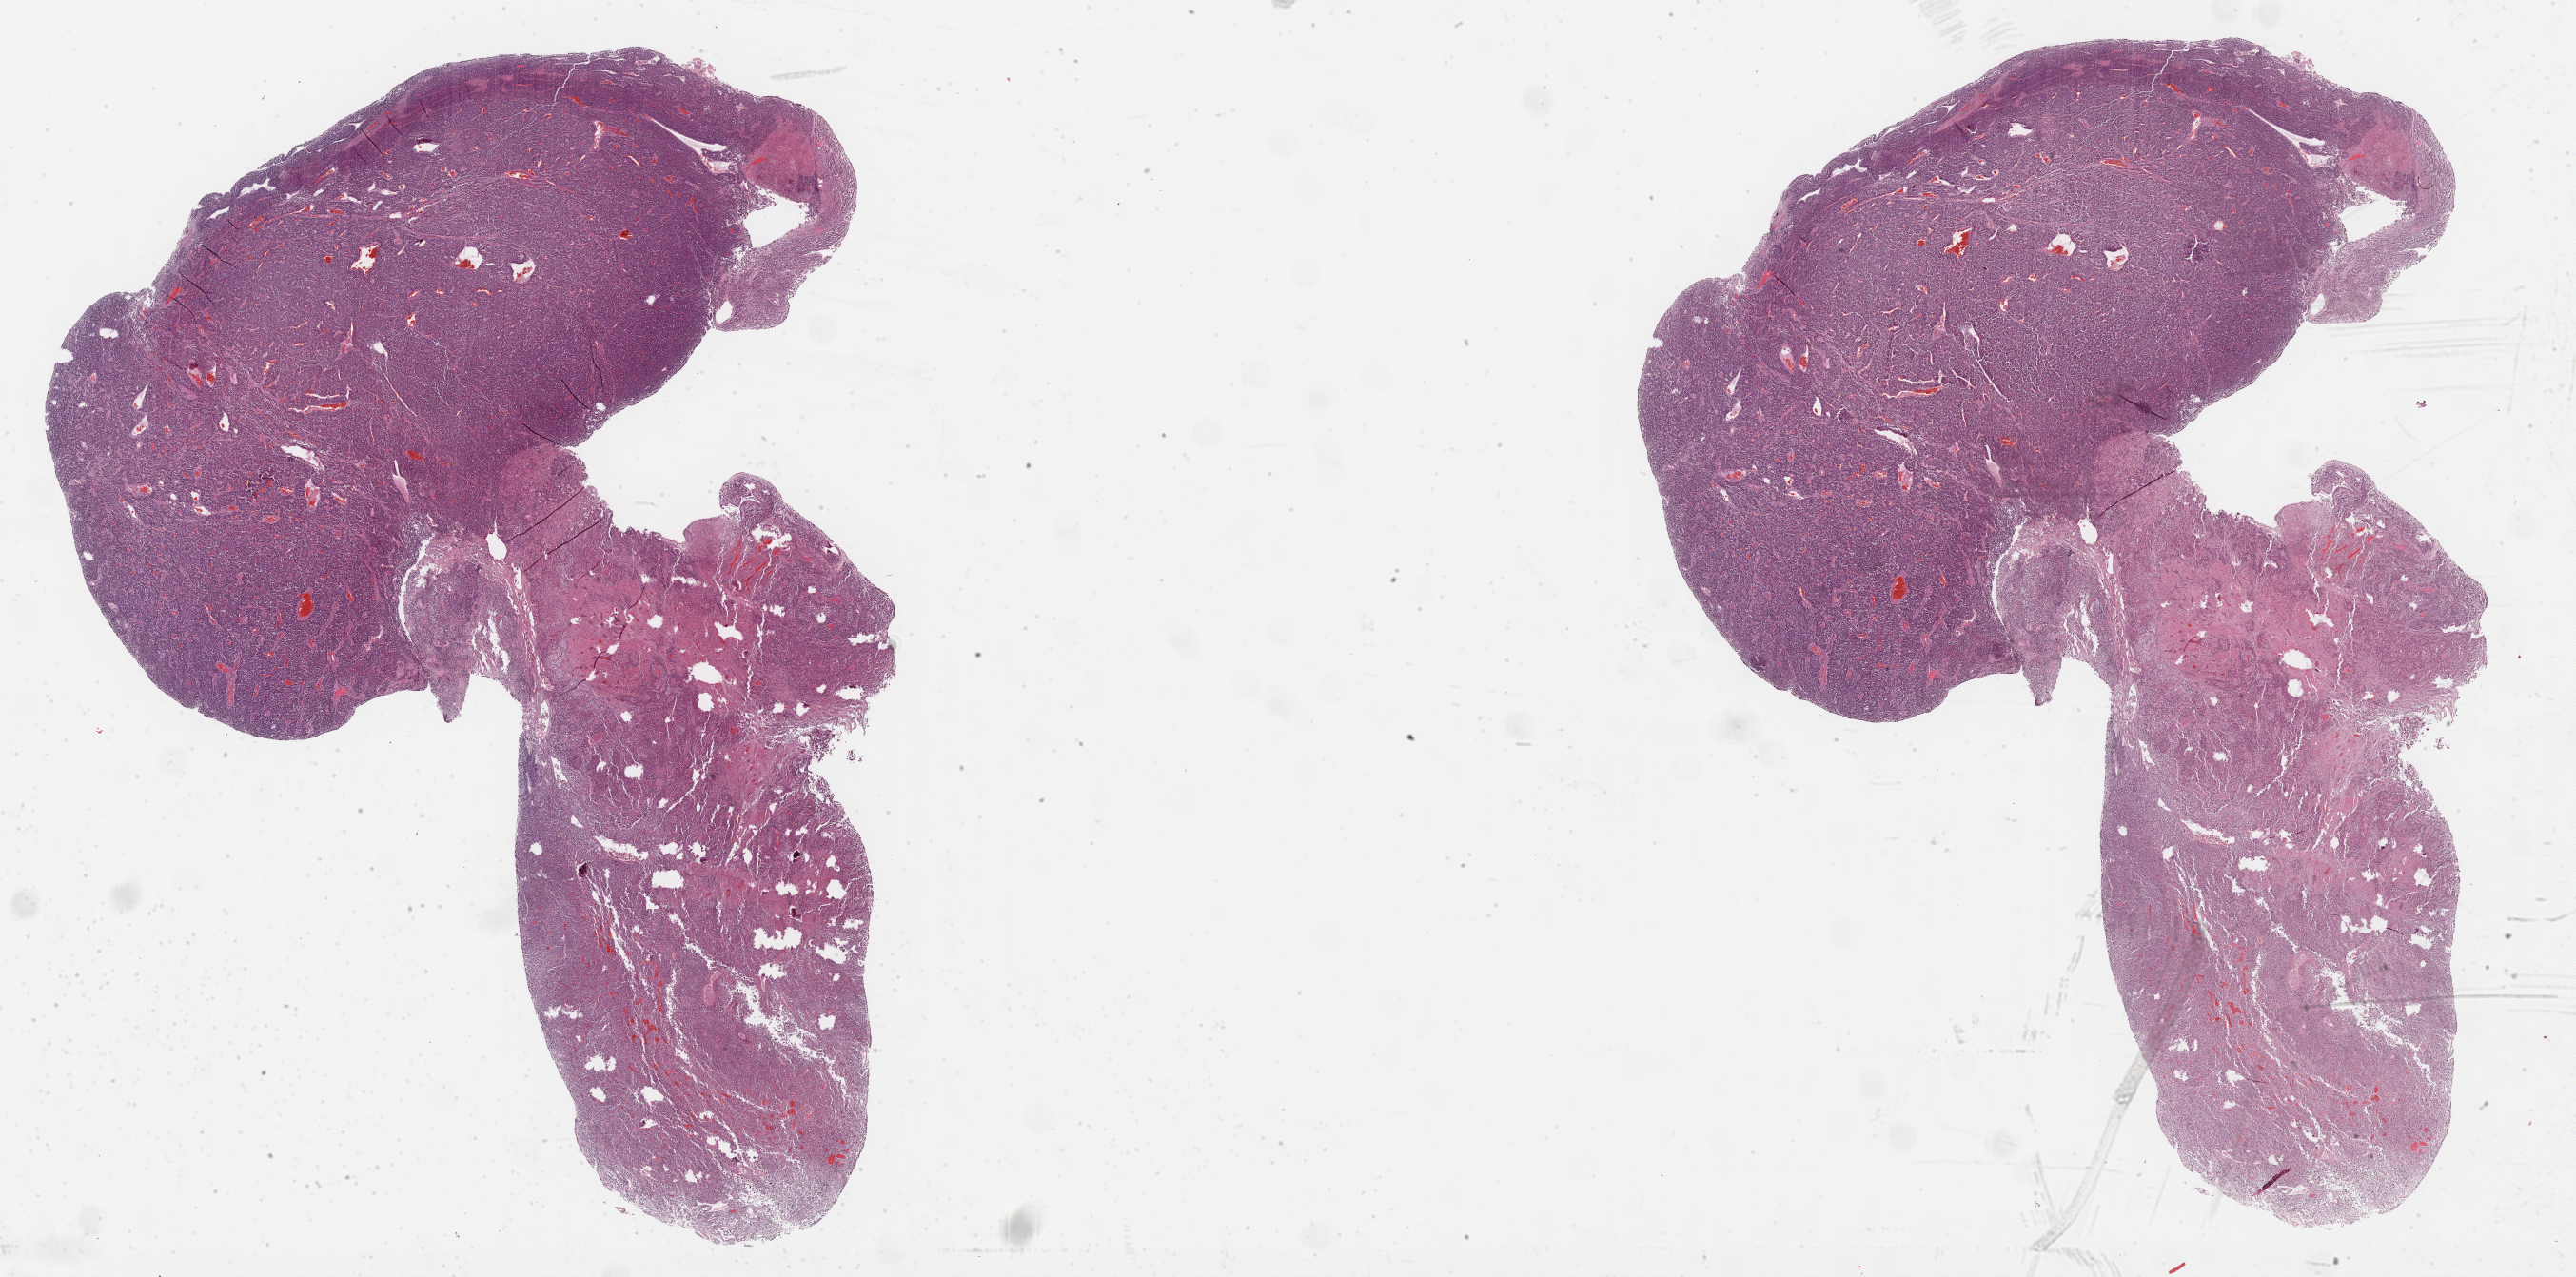
Whole-slide histology image, H&E, a low-resolution overview of the entire scanned area, about 43.8 x 21.7 mm (from a 40x scan). FFPE section. Primary tumour sample from the adrenal cortex. Female patient; age at initial diagnosis 32 years.
Histologic diagnosis: Adrenal cortical carcinoma (cortex of adrenal gland).